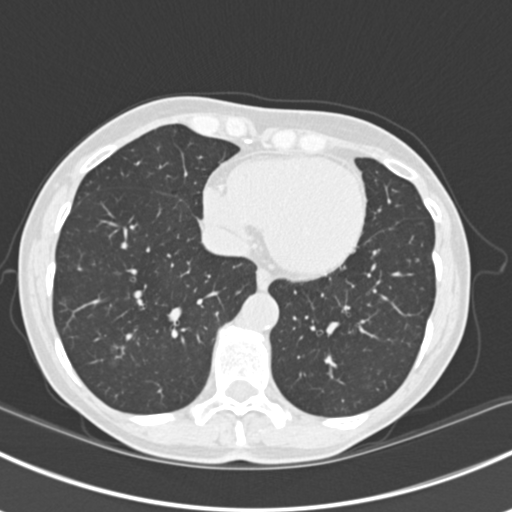
Chest CT (low-dose screening protocol), one axial image; baseline annual screen; lung window (W 1500 / L -600 HU); 2 mm slice thickness; 120 kVp; slice 135 of 224 in the series. Female, age 63 years at enrolment. Current smoker at enrolment.
- Expert reader's lesion annotation, bounding box (x1, y1, x2, y2) in pixels: (95, 329, 144, 372).
- The screening reader recorded 10 non-calcified nodules or masses ≥4 mm on this exam (right lower lobe, right lower lobe, left lower lobe, left lower lobe, right middle lobe, right lower lobe, left lower lobe, left upper lobe, right upper lobe, left upper lobe); which of them this box marks is not recorded.
- Participant outcome: lung cancer diagnosed 751 days after this screen — bronchiolo-alveolar adenocarcinoma, NOS, right upper lobe, right middle lobe, right lower lobe, left upper lobe, left lower lobe, moderately differentiated (G2), stage IV (AJCC 6th edition).